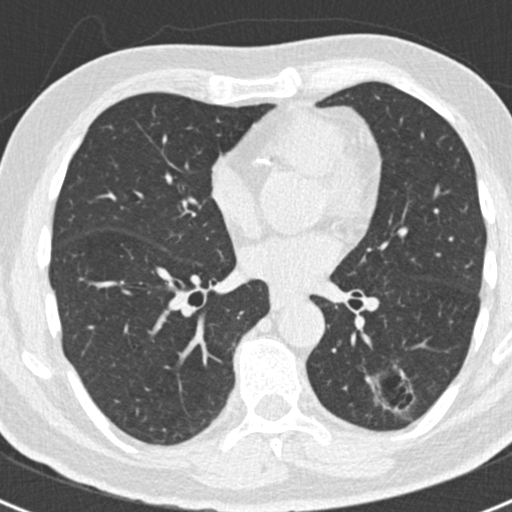
Axial slice from a low-dose chest CT screening exam; baseline annual screen; lung window (W 1500 / L -600 HU); 120 kVp; slice 92 of 188 in the series; 512 × 512 image matrix. Male, age 66 years at enrolment. Former smoker at enrolment.
- Expert-annotated lung lesion, bounding box <347,342,421,421> (left, top, right, bottom; pixels).
- Reader record for this screening exam (exam-level; its link to the box is not recorded): non-calcified nodule or mass ≥4 mm, left lower lobe, 43 × 27 mm, smooth margins.
- Official screen result: positive, change unspecified: nodule(s) >= 4 mm or enlarging nodule(s), mass(es), or other non-specific abnormalities suspicious for lung cancer.
- Participant outcome: lung cancer diagnosed 801 days after this screen (after the third annual screen) — adenocarcinoma, NOS, left lower lobe, poorly differentiated (G3), stage IB (AJCC 6th edition), 38 mm at pathology.